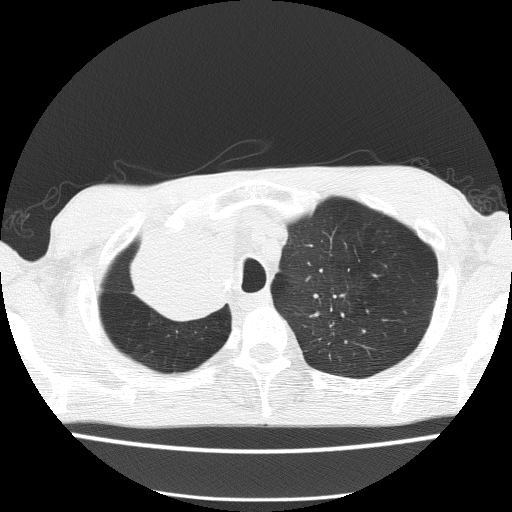
Chest CT (low-dose screening protocol), one axial image; first (baseline) screen; lung window (W 1500 / L -600 HU); 2 mm slice thickness; lung (sharp) reconstruction kernel (FC51). Male, age 59 years at enrolment. Former smoker at enrolment.
- Expert-annotated lung lesion, bounding box [x1, y1, x2, y2] px = [128, 236, 241, 328].
- The screening reader recorded 5 non-calcified nodules or masses ≥4 mm on this exam (left upper lobe, left upper lobe, left upper lobe, right middle lobe, right lower lobe); which of them this box marks is not recorded.
- Official screen result: positive, change unspecified: nodule(s) >= 4 mm or enlarging nodule(s), mass(es), or other non-specific abnormalities suspicious for lung cancer.
- Later outcome: lung cancer diagnosed 72 days after this screen — squamous cell carcinoma, NOS, right upper lobe, moderately differentiated (G2), stage IV (AJCC 6th edition).